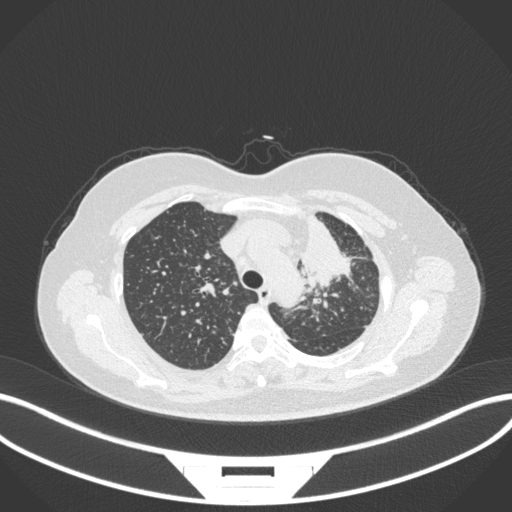
Chest CT, one axial slice; slice 255 of 348 in the series (ordered by position); reconstruction kernel B31f; 120 kVp; lung window (W 1500 / L -600 HU); 1 mm slice thickness; 512 × 512 image matrix, field of view 400 × 400 mm. Patient: female, 49 years. From the clinical record (not read from this slice): clinical TNM (as recorded): T1c N0 M1.
Annotated regions visible in this slice (rectangle marked by the reading radiologist):
- lung tumour (recorded histology: adenocarcinoma): bounding box <295,206,351,286> (left, top, right, bottom; pixels)